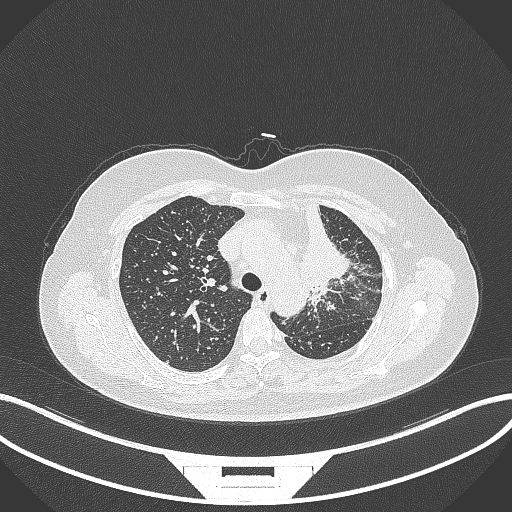
Chest CT, one axial slice. Slice 245 of 348 in the series (ordered by position). Lung window (W 1500 / L -600 HU). 512 × 512 image matrix. Female patient, age 49 years. From the clinical record (not read from this slice): clinical TNM (as recorded): T1c N0 M1.
Structures marked on this image (bounding box drawn by a radiologist):
- lung tumour (recorded histology: adenocarcinoma): bounding box (x1, y1, x2, y2) in pixels: (289, 197, 354, 297)